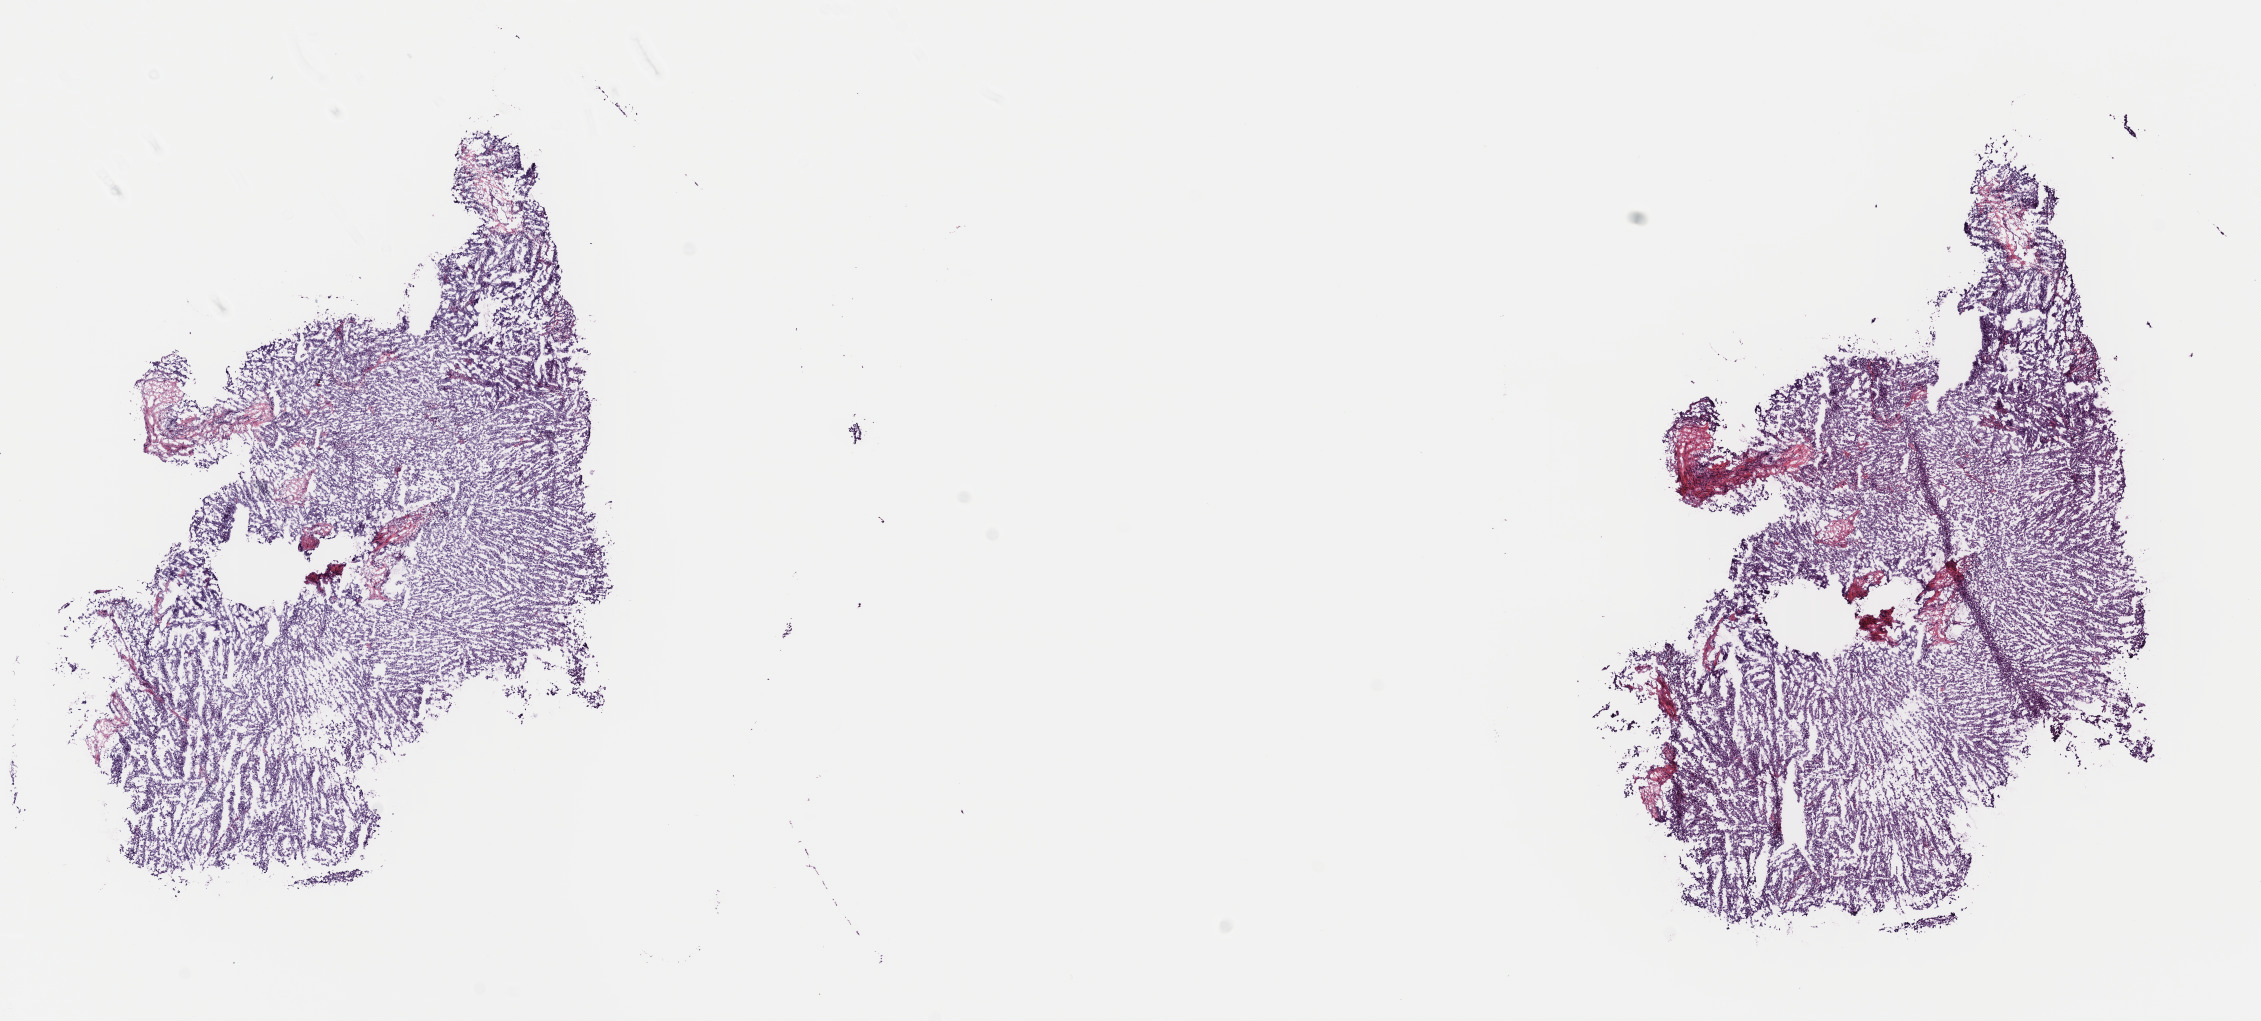
Digitized H&E-stained tissue section (whole slide), whole scanned area (about 17.8 x 8.1 mm) shown as a low-resolution overview; frozen section; sample: primary tumour, testis. Male, age 38 years at initial diagnosis. Slide review estimates, as recorded: tumour cells 95%, tumour nuclei 95%.
Diagnosis: Seminoma, NOS.